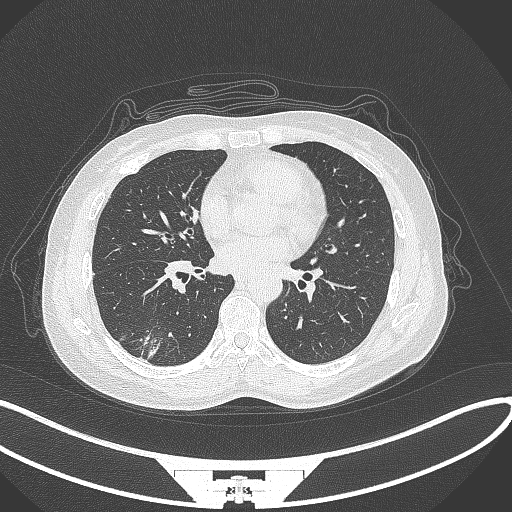
Chest CT, one axial slice; slice 132 of 352 in the series (ordered by position); 120 kVp; lung window (W 1500 / L -600 HU); 1 mm slice thickness; 512 × 512 image matrix, field of view 400 × 400 mm. Patient: female, 55 years. From the clinical record (not read from this slice): clinical TNM (as recorded): T1c N1 M0.
Annotated regions visible in this slice (bounding box drawn by a radiologist):
- lung tumour (recorded histology: adenocarcinoma): bounding box <137,324,162,364> (left, top, right, bottom; pixels)